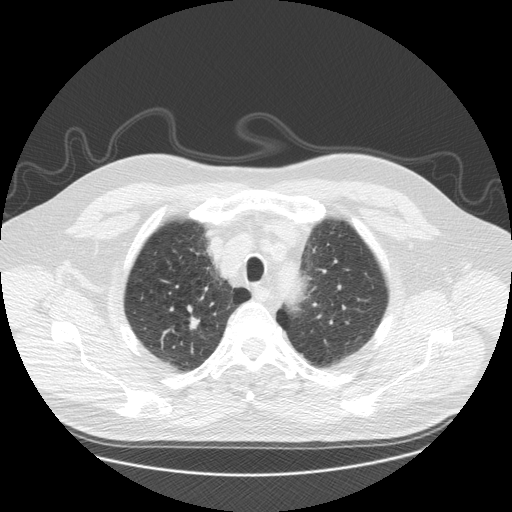
Low-dose screening chest CT, one axial slice. Position 145 of 173 along the scan axis. Reconstruction kernel STANDARD. Lung window (W 1500 / L -600 HU). 2.5 mm slice thickness. 512 × 512 image matrix, field of view 400 × 400 mm.
Annotated regions visible in this slice (expert manual segmentation):
- lesion 1 (tumor, upper lobe of right lung): bounding box (x1, y1, x2, y2) in pixels: (190, 317, 200, 330)